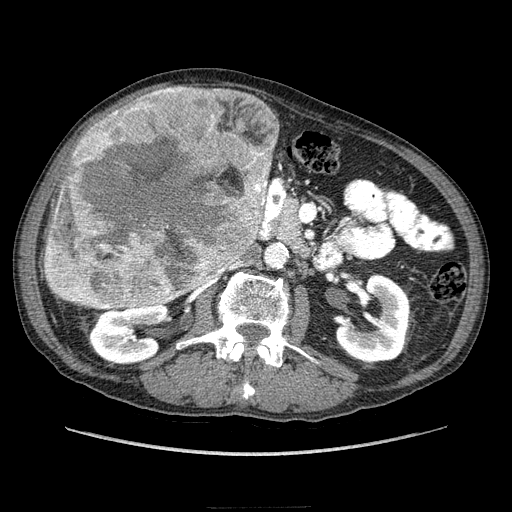
Contrast-enhanced abdominal CT (liver protocol), one axial slice; position 95 of 218 along the scan axis; 100 kVp; soft-tissue window (W 400 / L 40 HU); 2.5 mm slice thickness; 512 × 512 image matrix. Case-level facts recorded for this patient, not image findings: diagnosis: hepatocellular carcinoma (patient treated with transarterial chemoembolisation; whether this scan precedes or follows treatment is not stated here); TNM stage (as recorded): Stage-IIIA; Child-Pugh class: A; tumour nodularity: multinodular.
Structures marked on this image (semi-automatic segmentation, software-assisted and operator-edited):
- liver parenchyma outside the tumour (the mass and vessels are separate outlines, so this box may not span the whole liver): bounding box <74,92,278,152> (left, top, right, bottom; pixels)
- mass: <40,86,276,312>